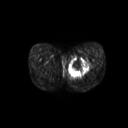
FDG PET of an extremity soft-tissue mass (from a PET/CT study), one axial slice. Position 30 of 267 along the scan axis. 128 × 128 image matrix, field of view 600 × 600 mm. Patient: male, 59 years. From the clinical record (not read from this slice): histological type: pleiomorphic liposarcoma; grade: high; site of the primary tumour: left thigh.
Structures marked on this image (expert contour drawn on MRI and transferred to this co-registered scan by the dataset authors):
- gross tumour volume including surrounding oedema: bounding box [x1, y1, x2, y2] px = [69, 57, 91, 78]
- gross tumour volume (mass): [70, 57, 90, 76]